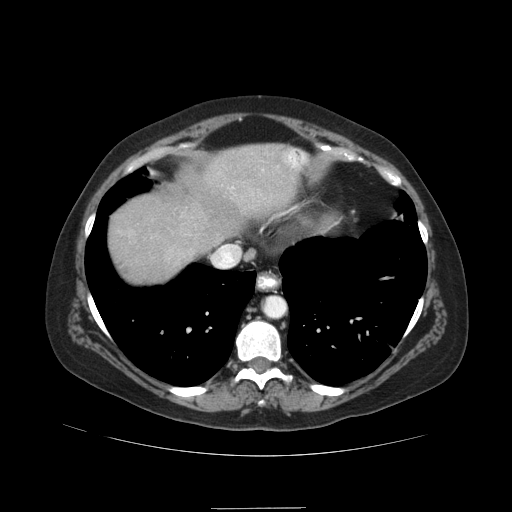
Contrast-enhanced abdominal CT (liver protocol), one axial slice; position 77 of 89 along the scan axis; reconstruction kernel STANDARD; soft-tissue window (W 400 / L 40 HU); 512 × 512 image matrix. From the clinical record (not read from this slice): diagnosis: hepatocellular carcinoma (patient treated with transarterial chemoembolisation; whether this scan precedes or follows treatment is not stated here); TNM stage (as recorded): Stage-IIIB; Child-Pugh class: A.
Outlined on this slice (semi-automatically segmented with operator editing):
- liver parenchyma outside the tumour (the mass and vessels are separate outlines, so this box may not span the whole liver): box from (x=108, y=144) to (x=298, y=282) px